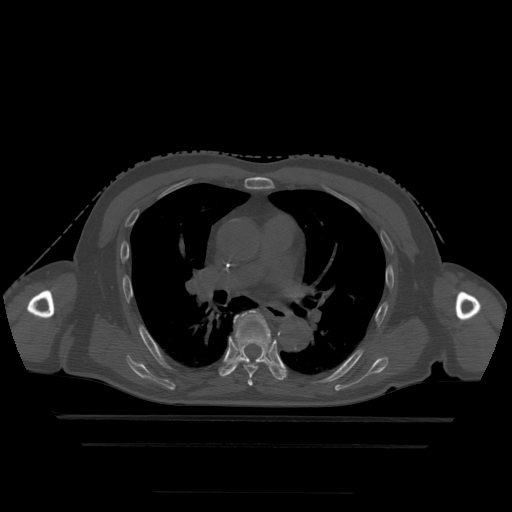
CT including the spine, one axial slice; slice 308 of 522 in the series (ordered by position); bone window (W 1800 / L 400 HU); 1.25 mm slice thickness; 512 × 512 image matrix, field of view 436 × 436 mm. Patient age 68 years. Case-level facts recorded for this patient, not image findings: primary cancer: urothelial.
Outlined on this slice (semi-automatic segmentation, software-assisted and operator-edited):
- T5 vertebra: bounding box (x1, y1, x2, y2) in pixels: (248, 375, 253, 386)
- T6 vertebra: (237, 311, 258, 378)
- T7 vertebra: (219, 311, 286, 381)